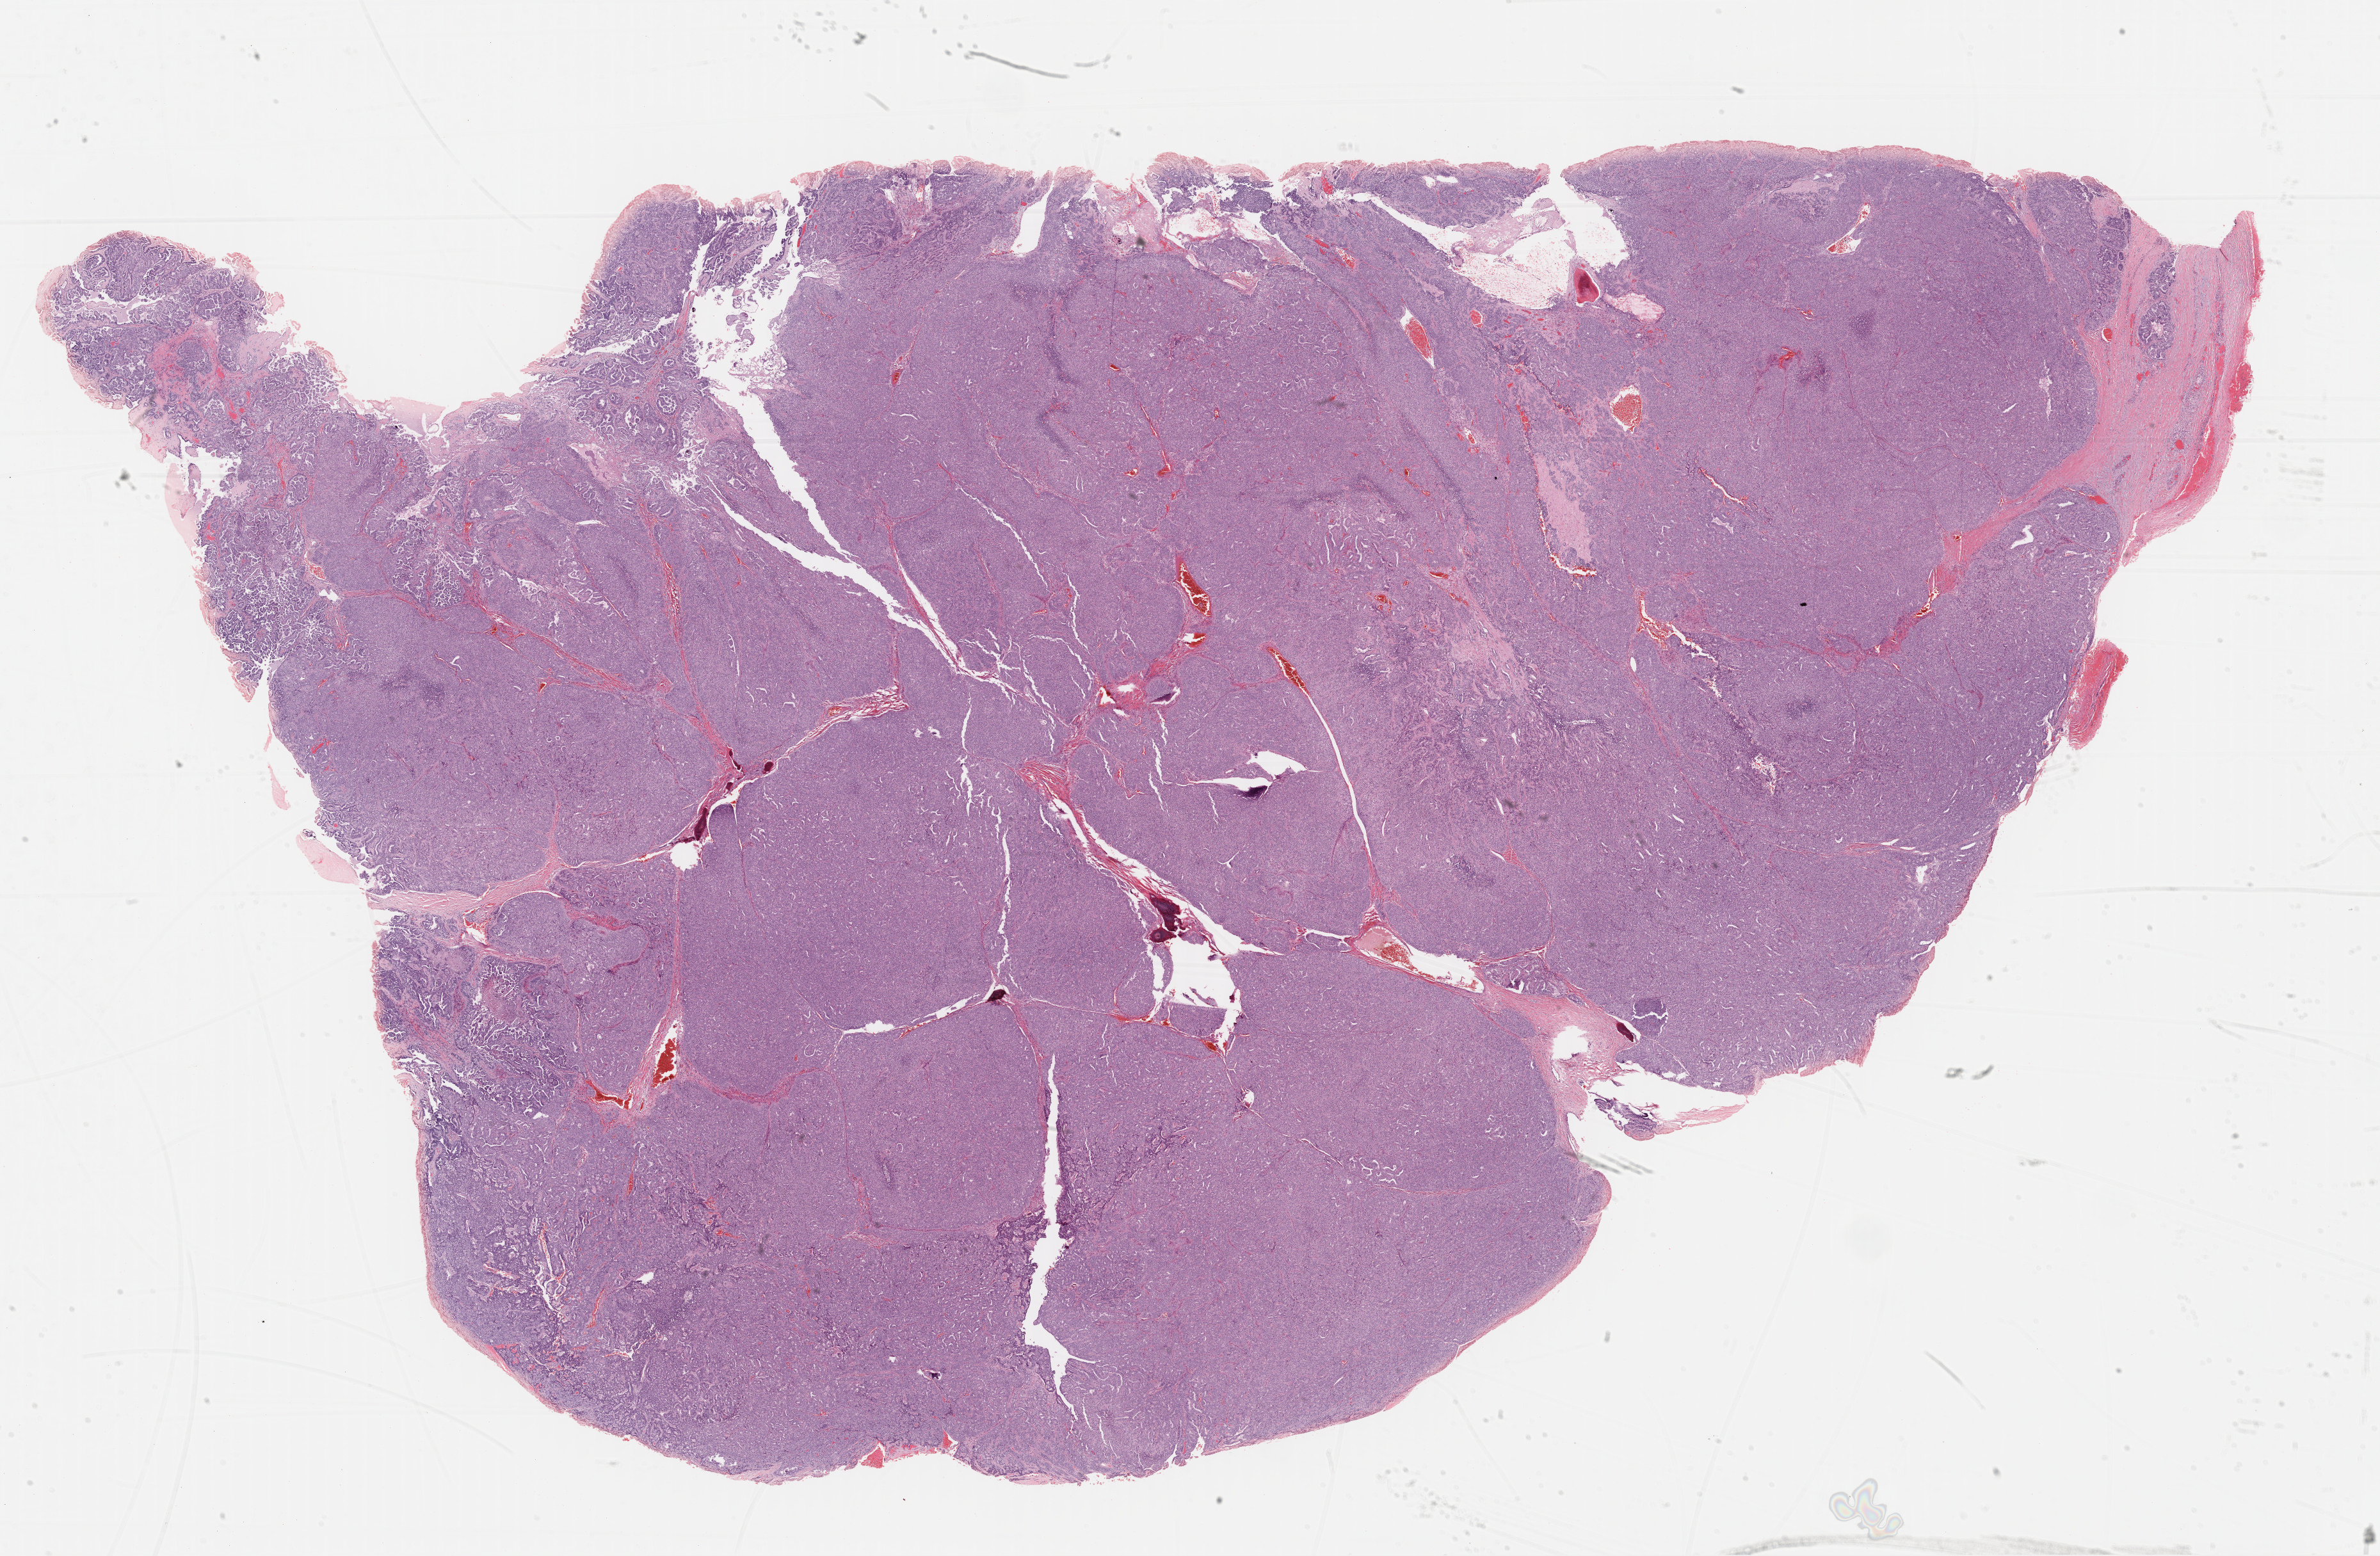
Hematoxylin and eosin (H&E) stained whole-slide image, shown as a low-resolution overview of the whole scanned area (about 29.2 x 19.1 mm). Formalin-fixed paraffin-embedded (FFPE) diagnostic section. Primary tumour sample from the thyroid. Female, age 66 years at initial diagnosis.
- pathologic diagnosis: Papillary adenocarcinoma, NOS (thyroid gland)
- lymph nodes positive (case pathology): 0 of 2 examined
- AJCC pathologic stage: IVC (6th edition)
- laterality: left